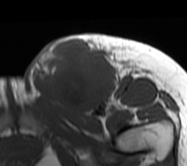
MRI of an extremity soft-tissue mass, one axial slice; position 30 of 62 along the scan axis; MR volume resampled by the dataset authors to the PET/CT grid (not the native acquisition matrix); 3.27 mm slice thickness; 187 × 166 image matrix. Female patient. Case-level facts recorded for this patient, not image findings: histological type: leiomyosarcoma; grade: high; site of the primary tumour: groin.
Annotated regions visible in this slice (expert contour drawn on MRI and transferred to this co-registered scan by the dataset authors):
- gross tumour volume including surrounding oedema: box from (x=25, y=33) to (x=138, y=118) px
- gross tumour volume (mass): (x=30, y=39)–(x=117, y=116)